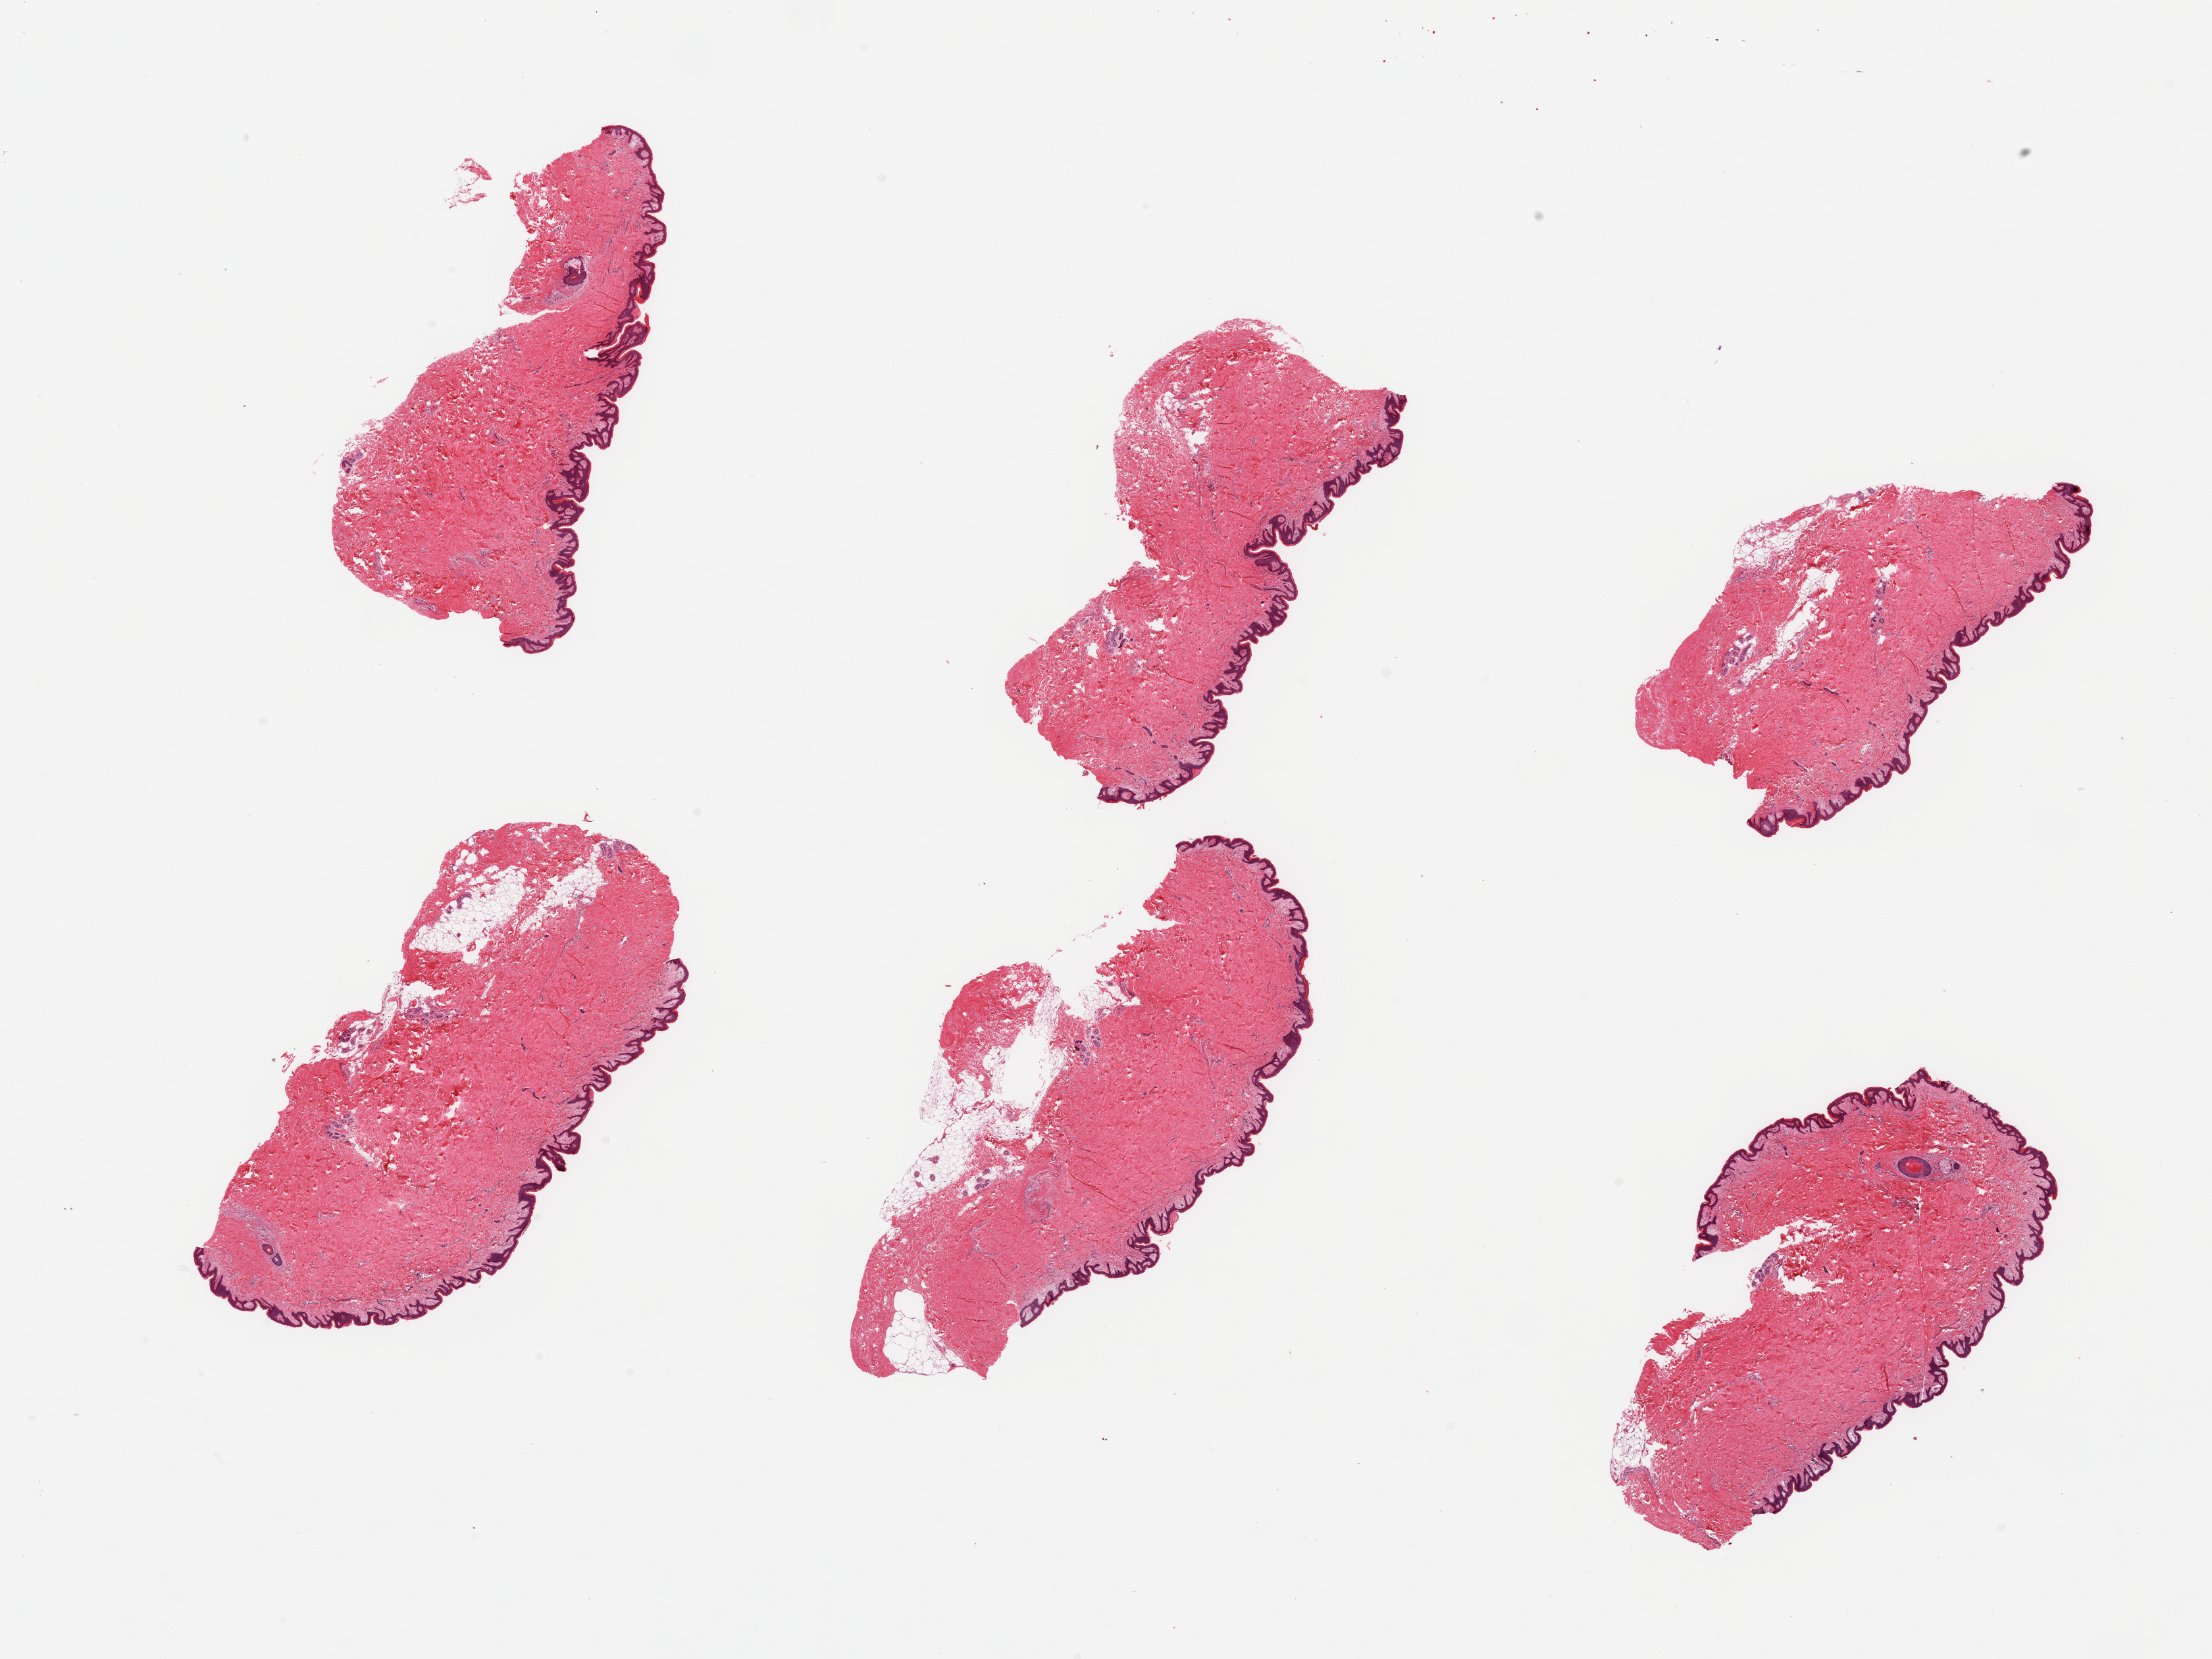
Digitized H&E-stained section, shown as a low-resolution overview of the whole scanned area (about 26.6 x 19.9 mm); PAXgene-fixed paraffin-embedded (PFPE) section; target tissue: skin of suprapubic region; donor tissue sample. Donor sex: male.
• pathologist's review note for this sample: 6 pieces, trace dermal fat; squamous epithelium is ~40 microns